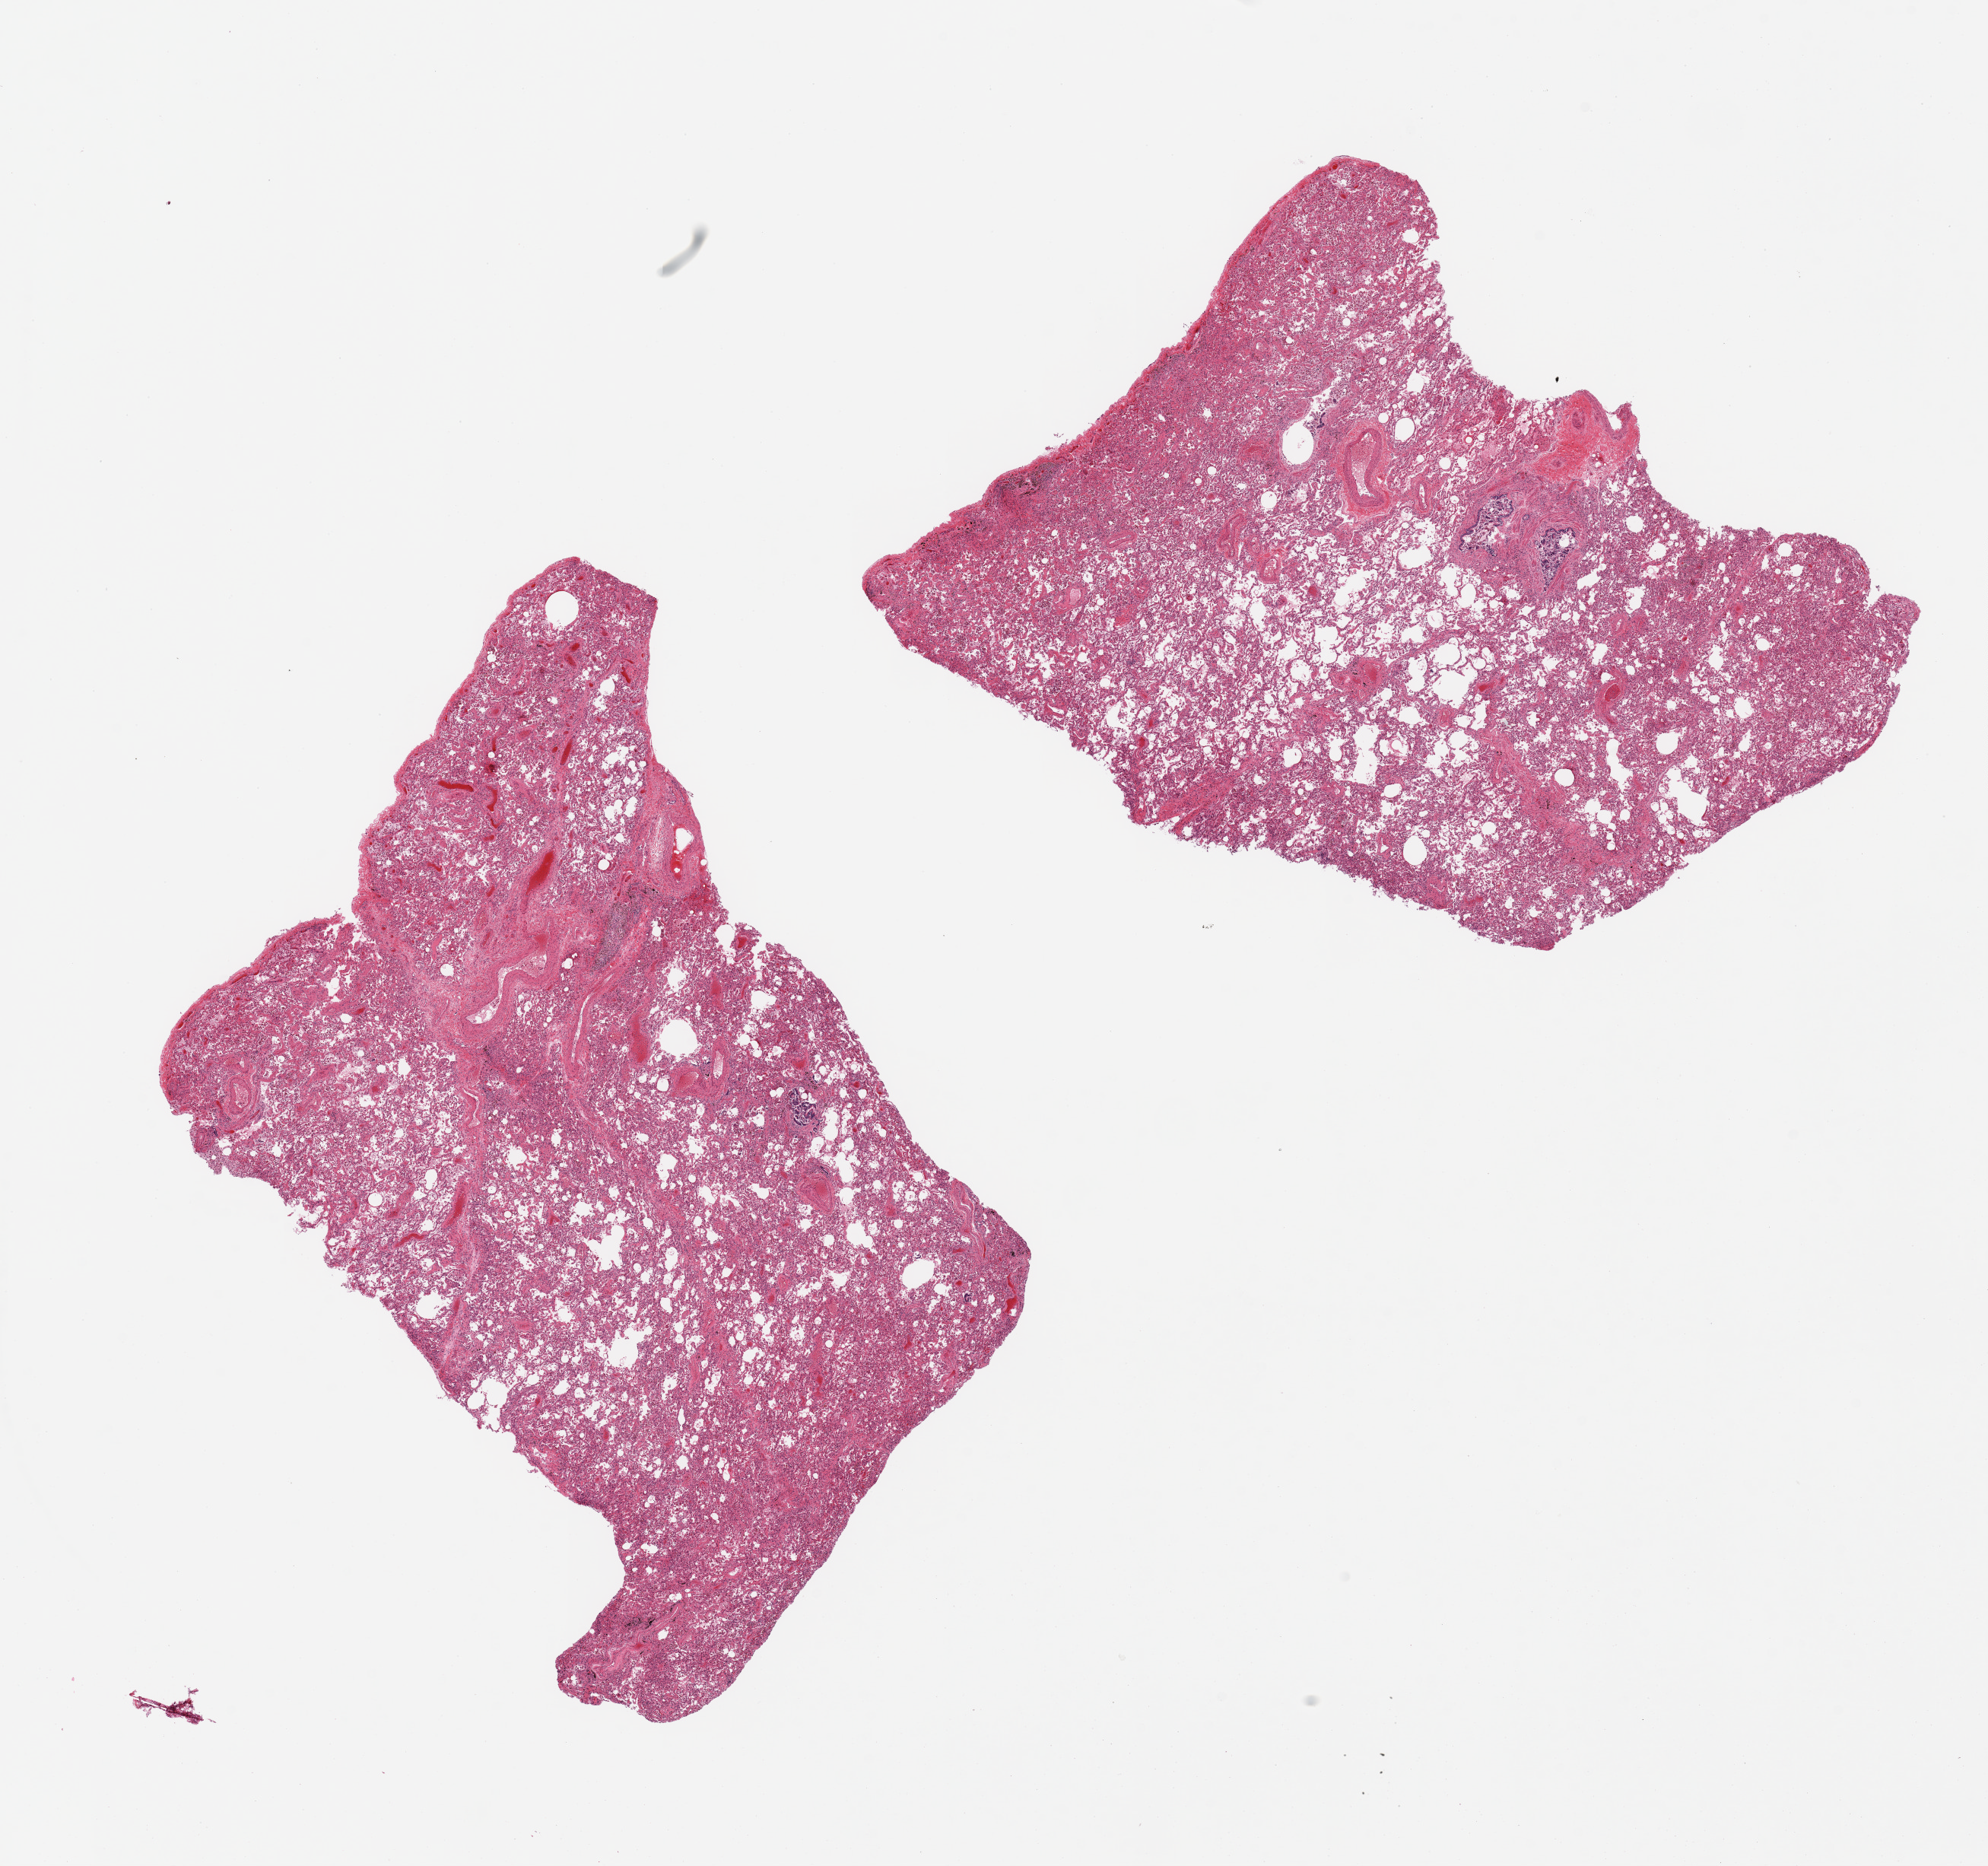
Haematoxylin and eosin whole-slide image — low-resolution overview of the scanned area, about 20.7 x 19.4 mm (slide scanned at 20x); PAXgene-fixed paraffin-embedded (PFPE) section; sampled site (target tissue): lung; tissue donor sample. Donor sex: male.
Review note (as recorded): 2 pieces. Patchy fibrosis and heart failure cells.